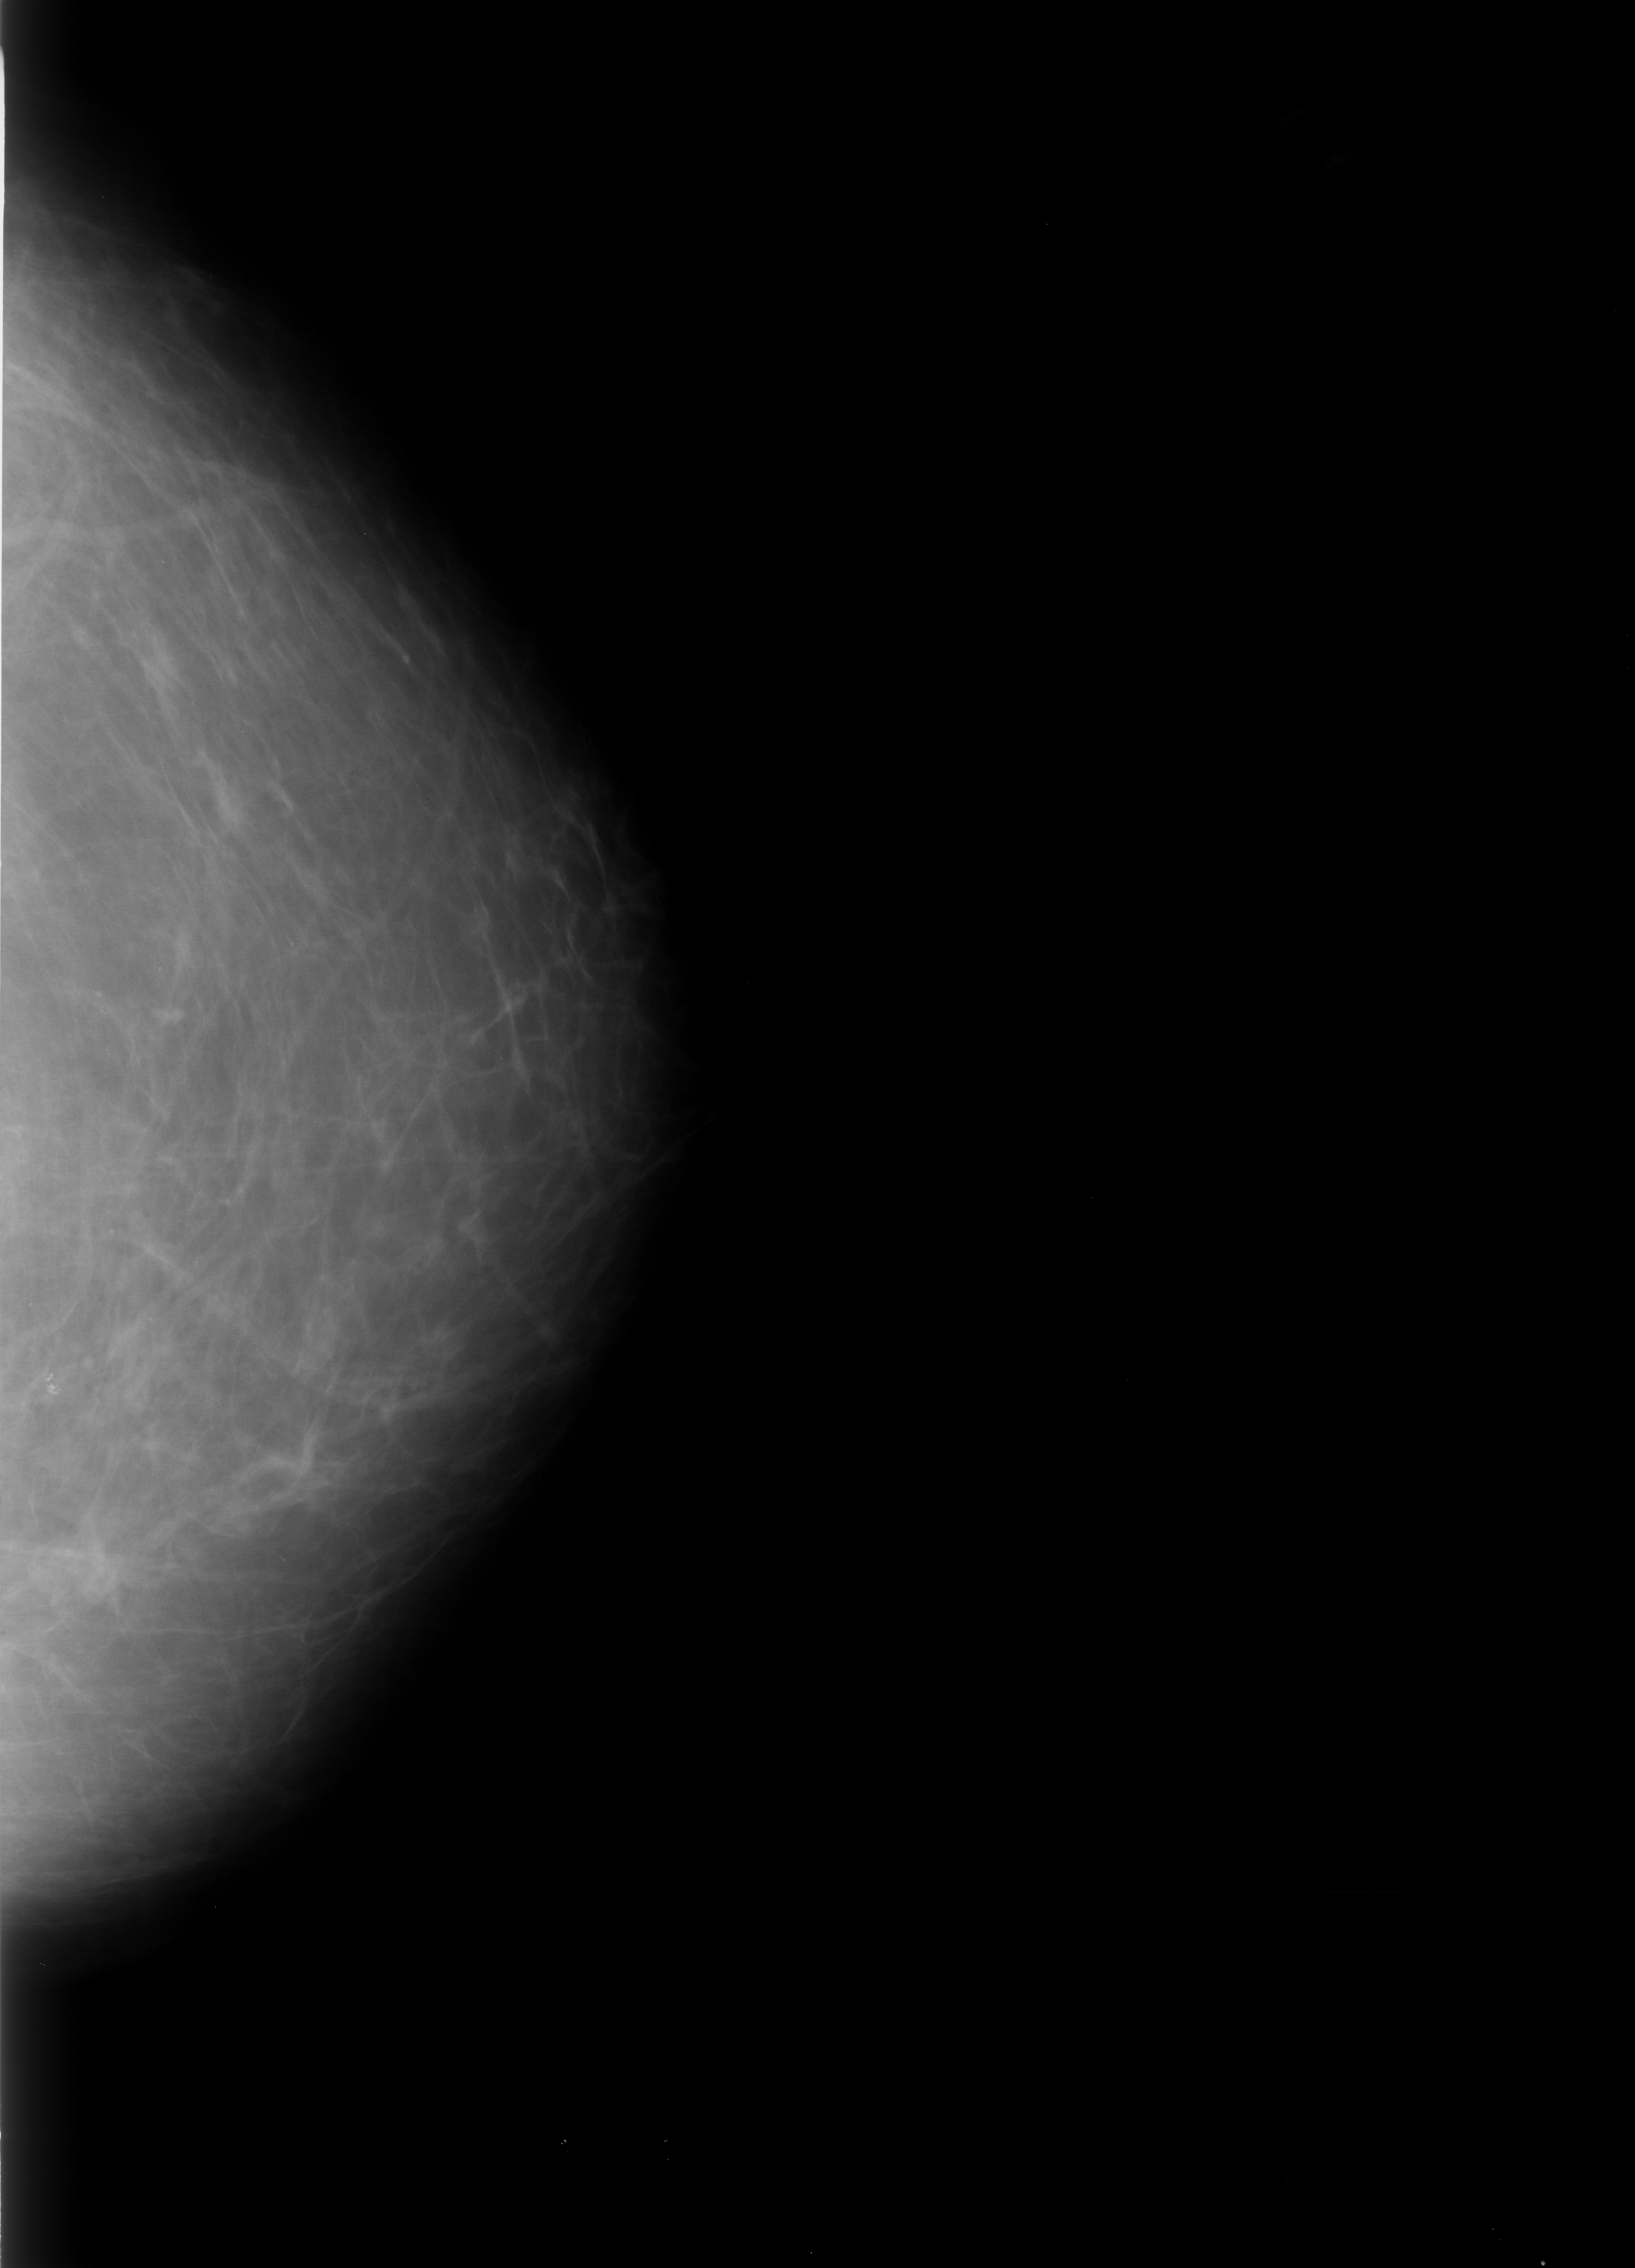
Mammogram (digitized film); left breast; craniocaudal (CC) view; BI-RADS breast density category 1 (scale 1–4).
- Marked findings (only marked abnormalities are described; nothing is implied about the rest of the image): calcifications, morphology pleomorphic, distribution clustered; BI-RADS assessment category 4; subtlety rating 4 on a 1 (subtle) to 5 (obvious) scale; pathology result (as recorded, not read from the image): benign.